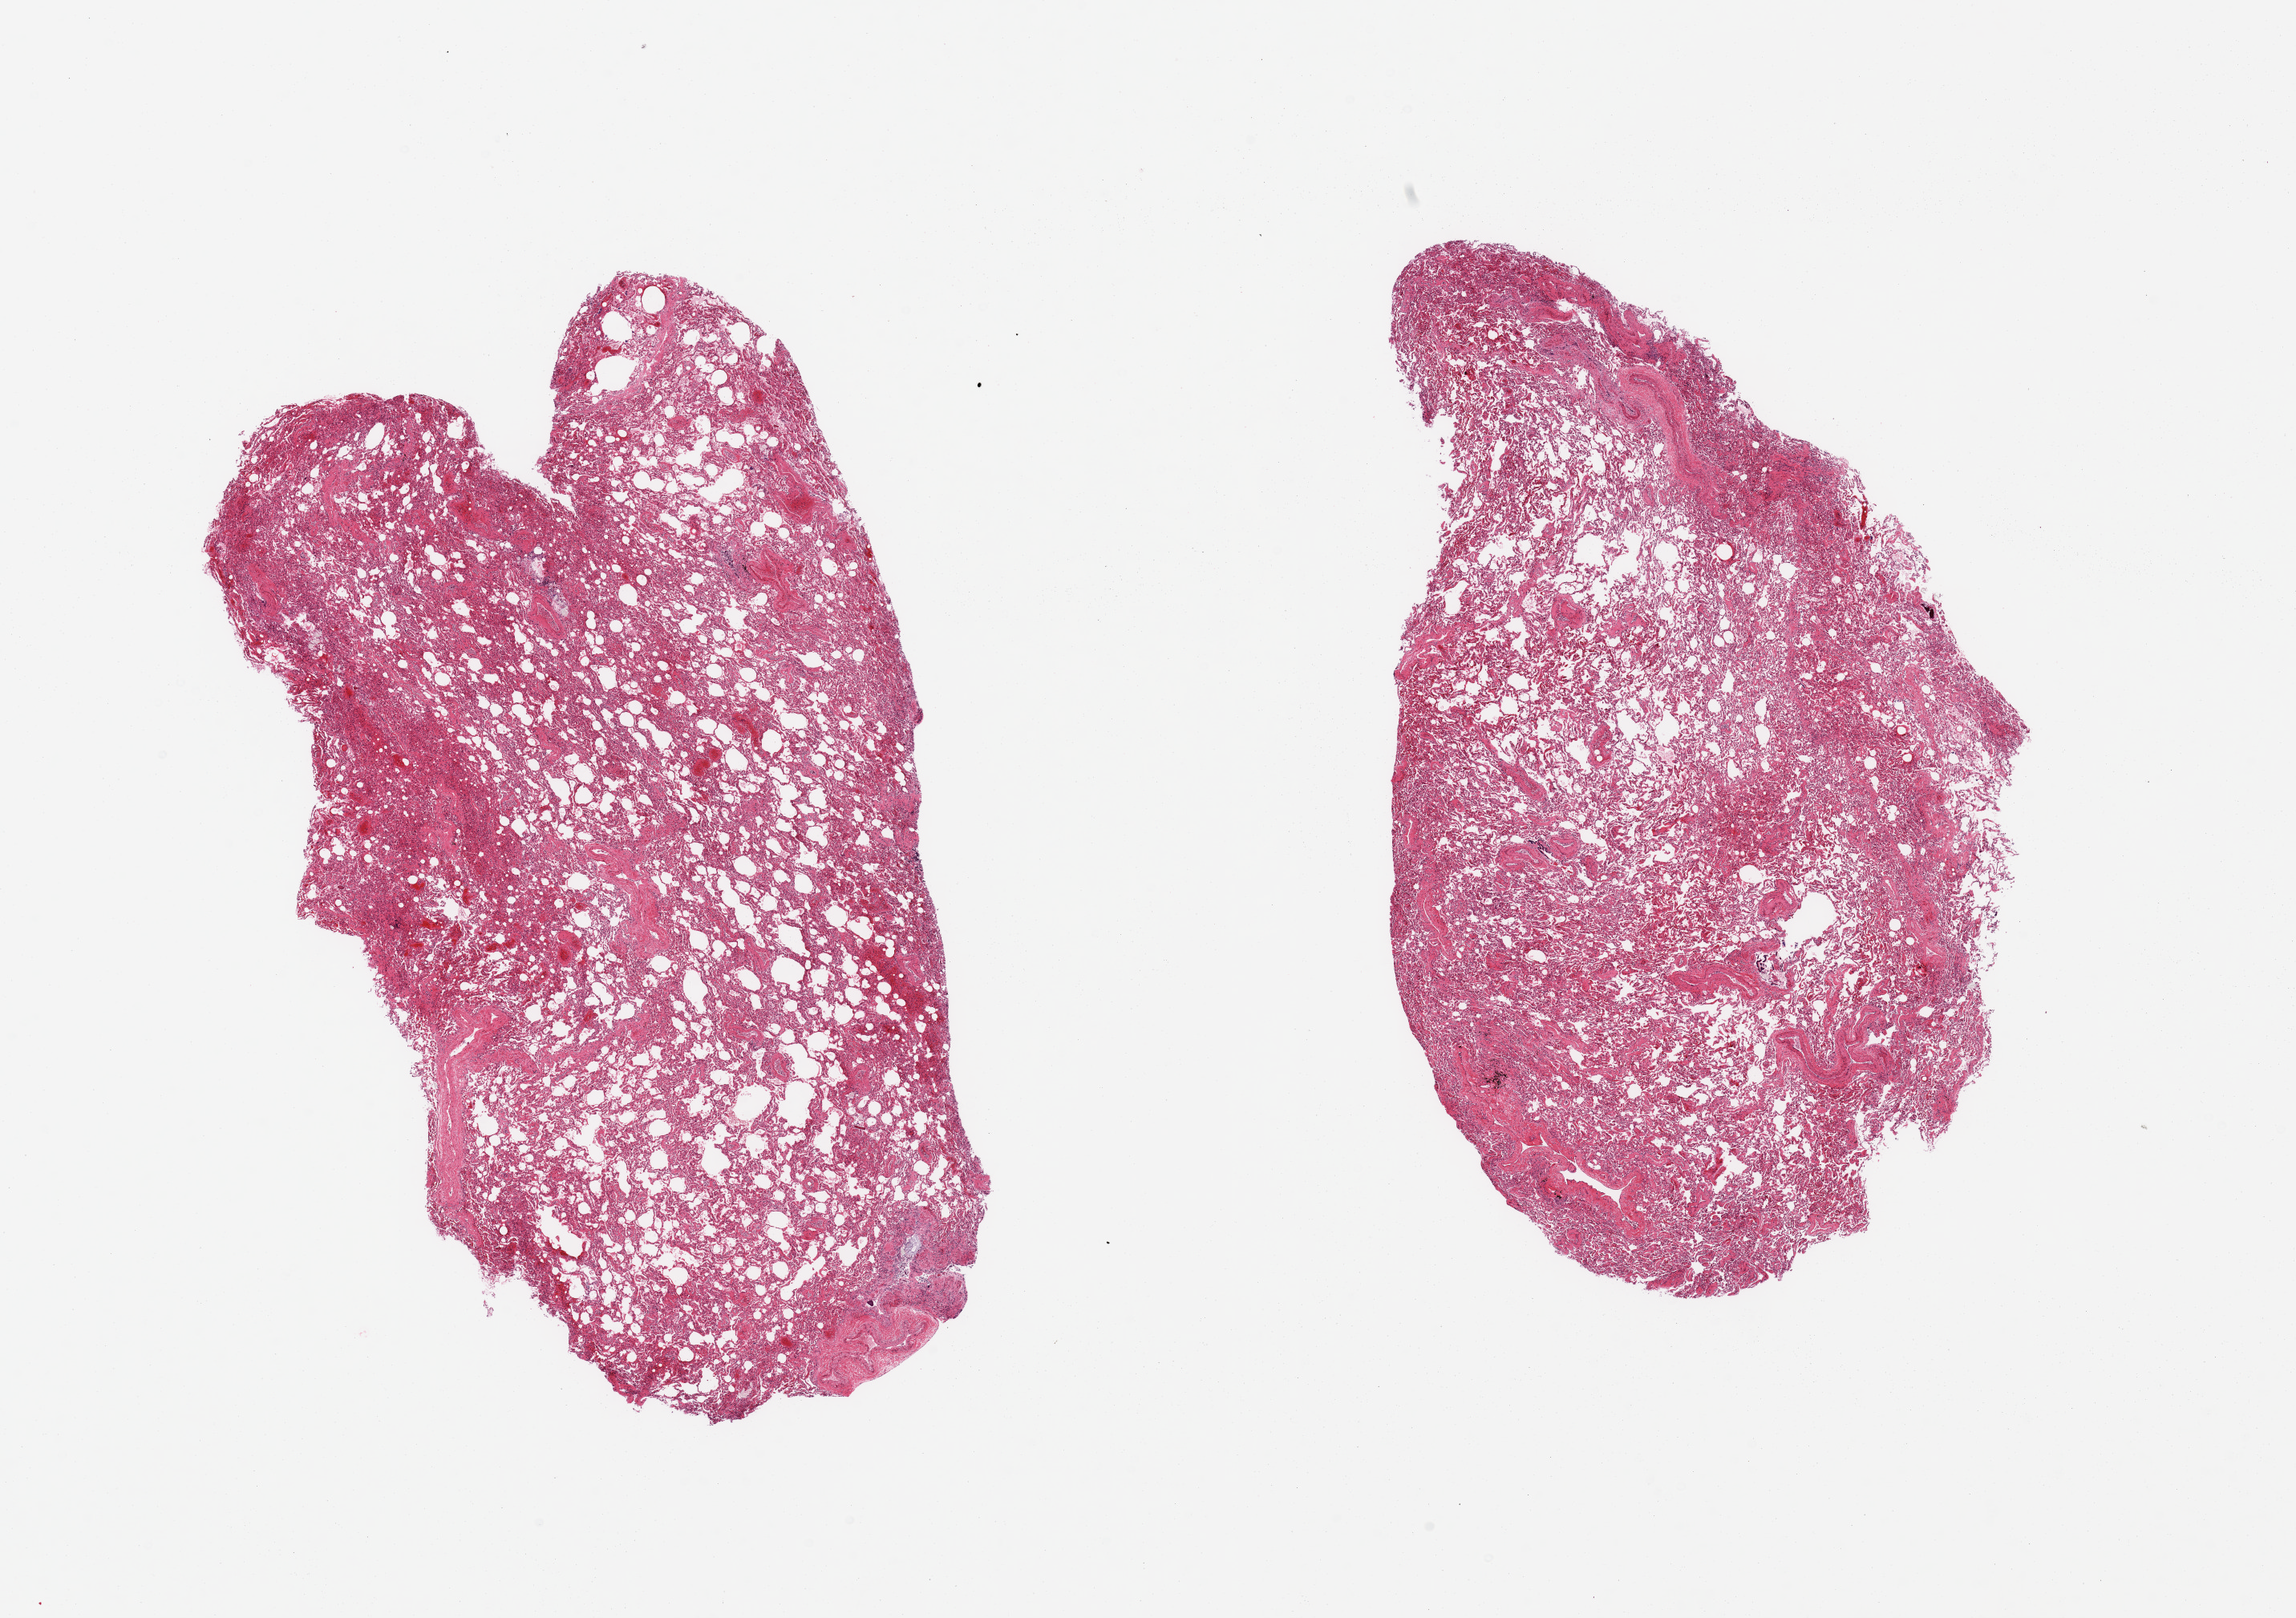
Haematoxylin and eosin whole-slide image — low-resolution overview of the scanned area, about 22.6 x 16.0 mm (from a 20x scan), PAXgene-fixed paraffin-embedded (PFPE) section, section of lung (target tissue), tissue donor sample. Donor: male.
• review note (as recorded): 2 pieces; mild to moderate autolysis; marked congestion; patchy intralveolar neutrophils, mucous, bacterial colonization (pneumonia) and aspirated foreign material; thick walled vessels